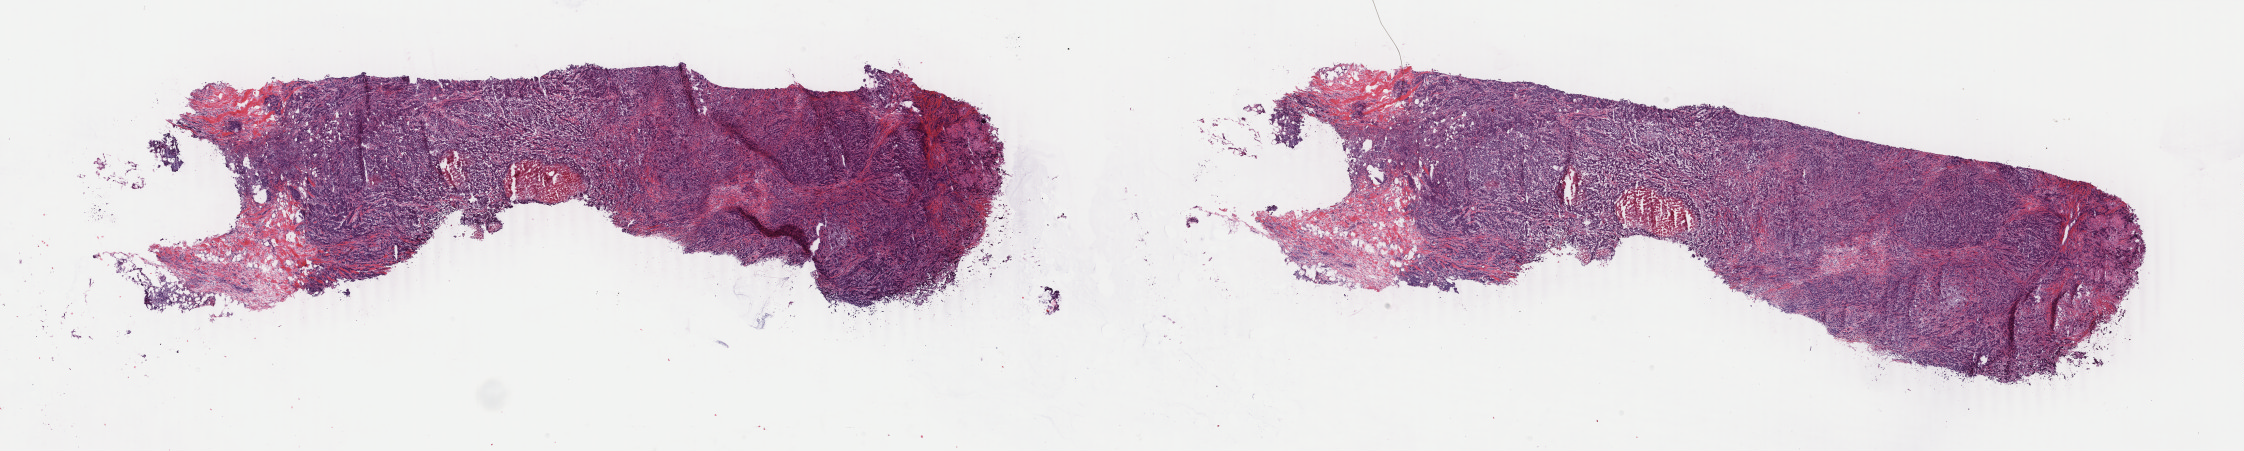
Whole-slide histology image, H&E, low-resolution overview of the scanned area, about 35.7 x 7.2 mm, frozen section from the top of the tissue portion, sample: primary tumour, breast. Female, age 63 years at initial diagnosis. Slide review estimates, as recorded: tumour cells 80%, tumour nuclei 90%, normal cells 1%, stromal cells 13%, necrosis 6%. Inflammatory infiltration, as recorded: lymphocyte infiltration 2%, monocyte infiltration 0%, neutrophil infiltration 1%.
Diagnosis: Infiltrating duct carcinoma, NOS. Lymph nodes positive (case pathology): 8 of 9 examined. AJCC pathologic stage: IV (6th edition).